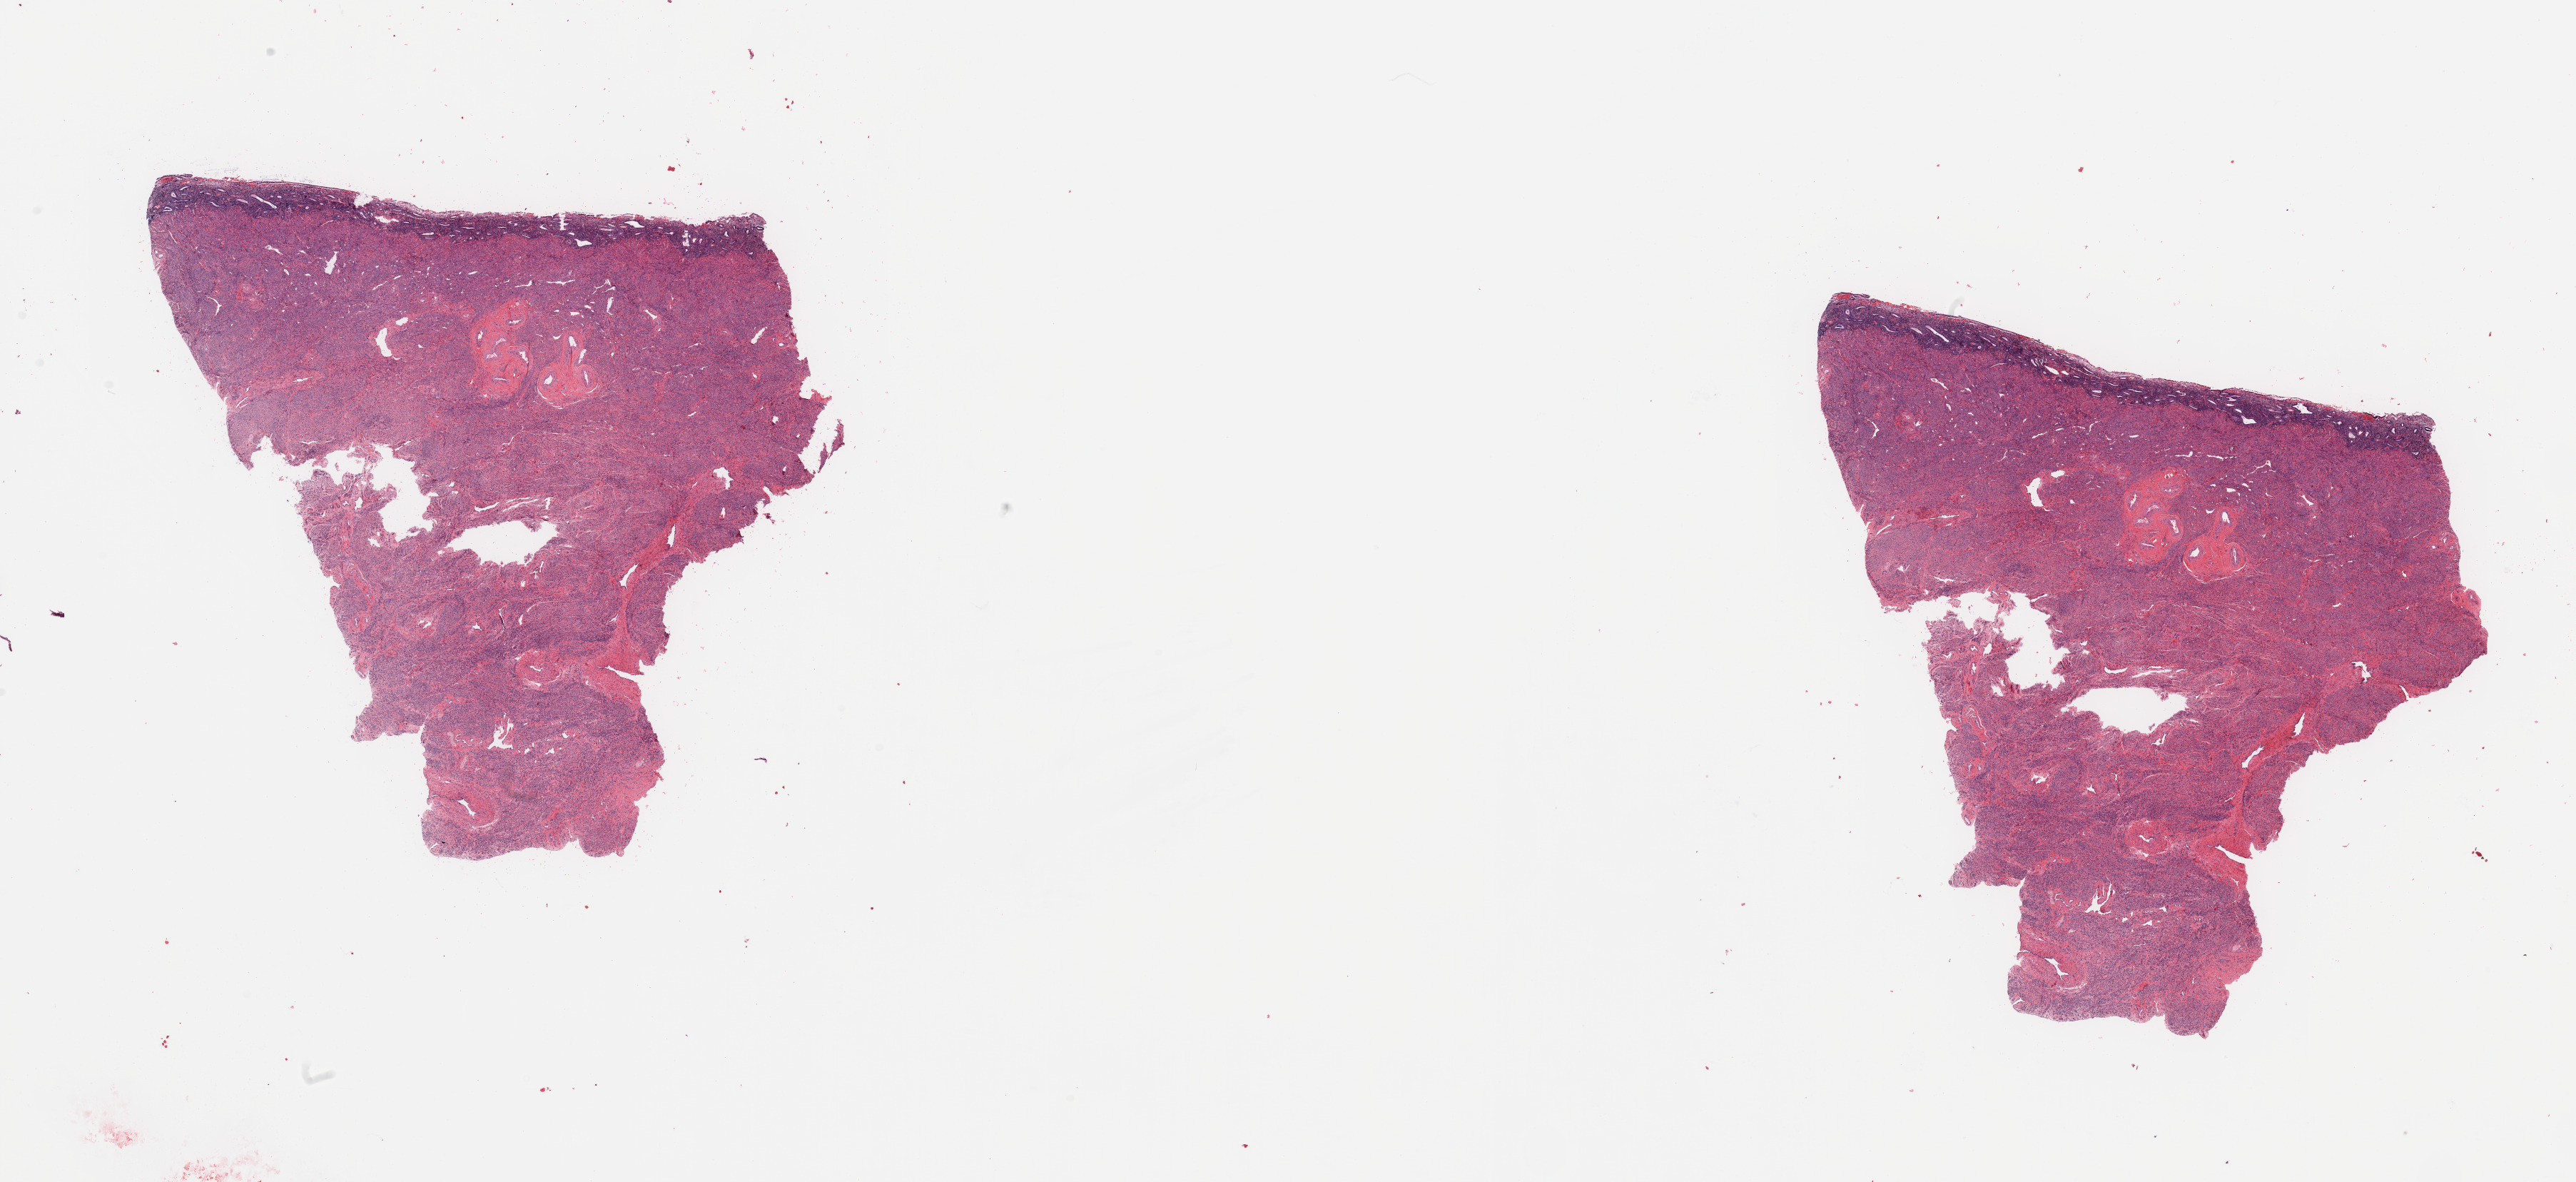
Whole-slide histology image, H&E-stained — low-resolution overview of the scanned area, about 28.5 x 13.1 mm (acquisition: 20x scan); normal (non-tumour) tissue sample, sampled site: uterus. Female, 53 y/o.
• this section: normal (non-tumour) tissue from the same patient
• patient diagnosis: Endometrioid adenocarcinoma, NOS